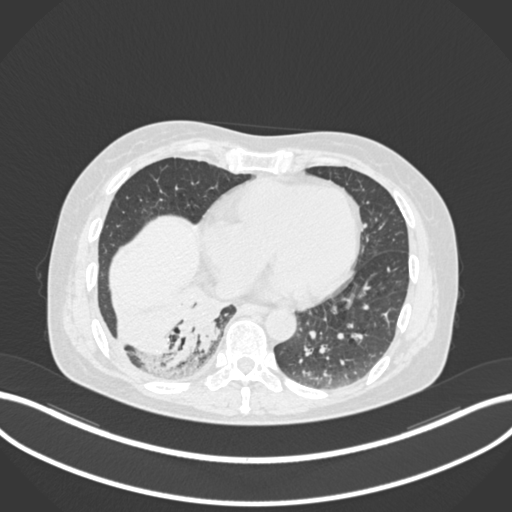
Chest CT, one axial slice; position 46 of 168 along the scan axis; reconstruction kernel B30f; lung window (W 1500 / L -600 HU); 1 mm slice thickness; 512 × 512 image matrix, field of view 400 × 400 mm. Female patient, age 63 years. From the clinical record (not read from this slice): clinical TNM (as recorded): T1c N0 M0.
Structures marked on this image (bounding box drawn by a radiologist):
- lung tumour (recorded histology: adenocarcinoma): bounding box [x1, y1, x2, y2] px = [170, 291, 226, 365]